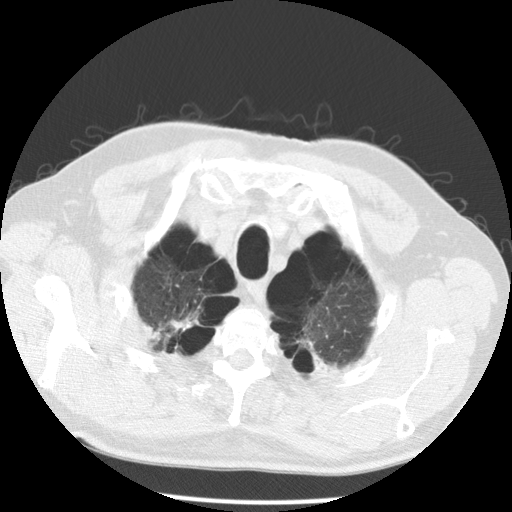
Chest CT (low-dose screening protocol), one axial image. Second annual screen. Lung window (W 1500 / L -600 HU). 2.5 mm slice thickness. Standard (soft-tissue) reconstruction kernel (STANDARD). 120 kVp. Male participant, aged 68 years at enrolment. Former smoker at enrolment.
Lesion marked by an expert reader, bounding box [x1, y1, x2, y2] px = [129, 290, 204, 362]. The screening reader recorded 2 non-calcified nodules or masses ≥4 mm on this exam; which of them this box marks is not recorded. Official screen result: positive, no significant change: stable abnormalities potentially related to lung cancer, unchanged since the prior screening exam. Lung cancer was diagnosed 617 days after this screen: large cell carcinoma, NOS, right upper lobe, poorly differentiated (G3), stage IV (AJCC 6th edition).